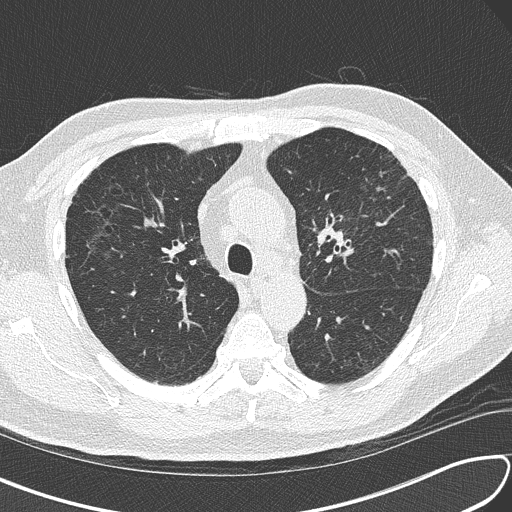
Chest CT (low-dose screening protocol), one axial image, third annual screen, lung window (W 1500 / L -600 HU), slice 48 of 156 in the series, 512 × 512 image matrix. Male, age 67 years at enrolment. Current smoker at enrolment.
- Expert-annotated lung lesion, box from (x=300, y=182) to (x=402, y=280) px.
- The exam's reader record, not a measurement of the box and not confirmed to be the same lesion: non-calcified nodule or mass ≥4 mm, left upper lobe, 30 × 23 mm, soft tissue attenuation, pre-existing on the prior screen: no.